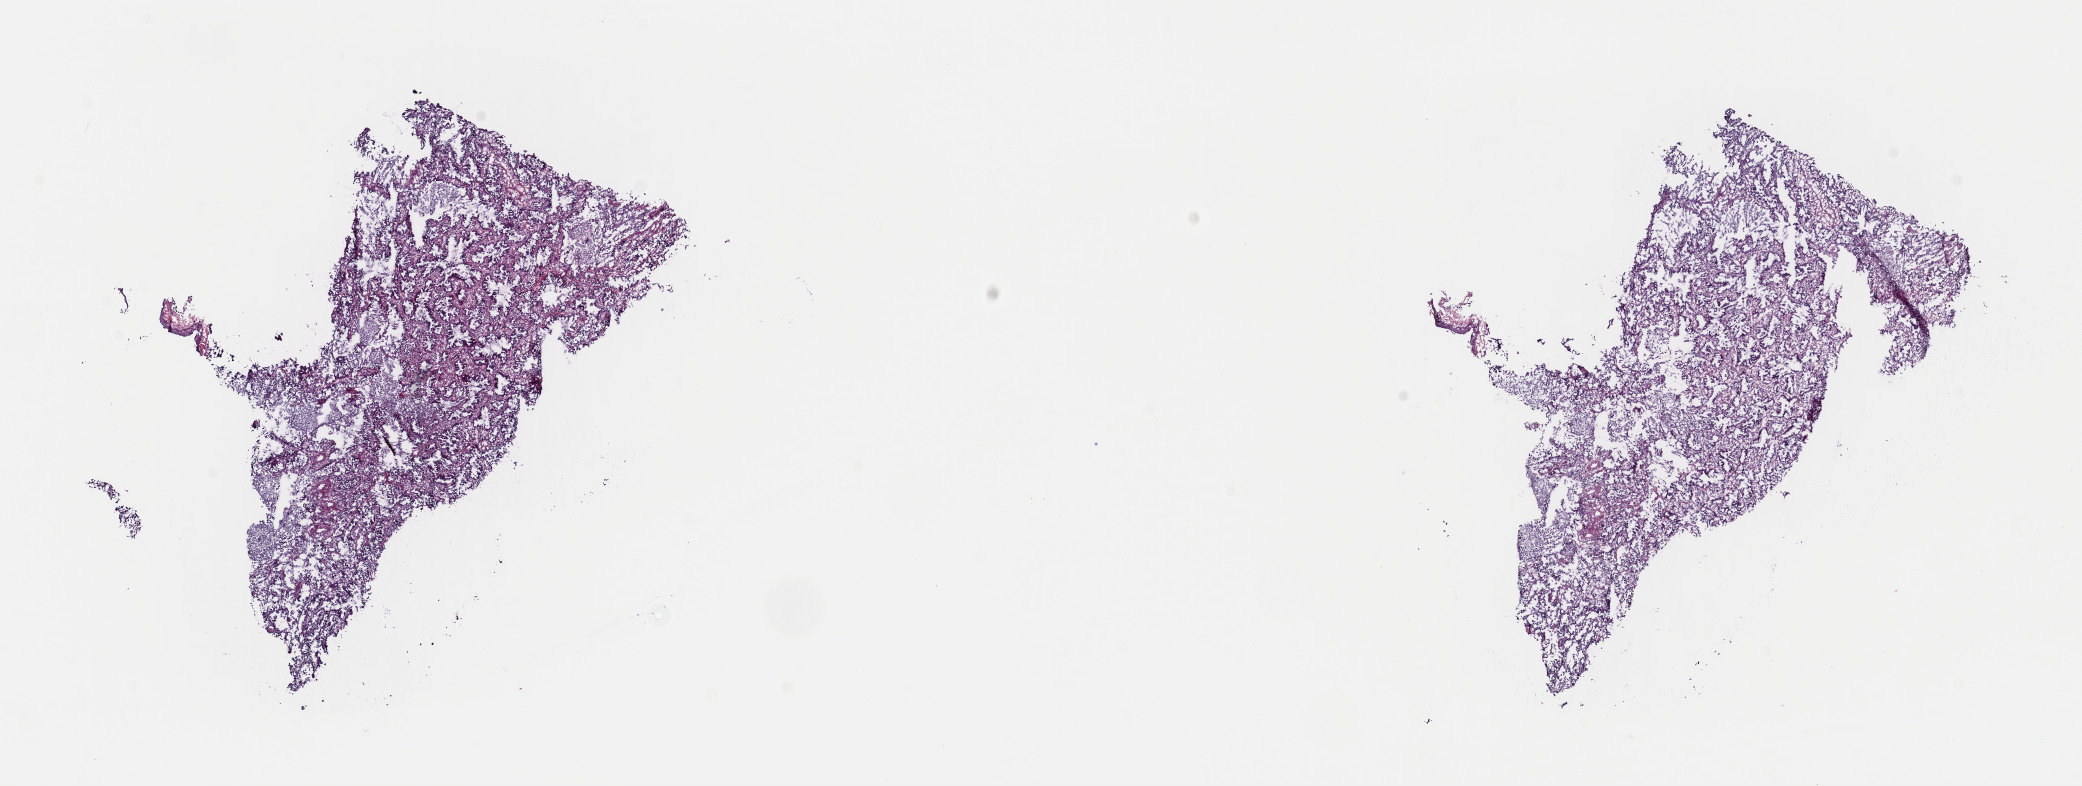
Digitized H&E-stained tissue section (whole slide) — shown as a low-resolution overview of the whole scanned area (about 16.4 x 6.2 mm). Frozen section from the top of the tissue portion. Sample: primary tumour, lung. Patient: female, age at initial diagnosis 74 years. Slide review estimates, as recorded: tumour cells 100%, tumour nuclei 75%, normal cells 0%, stromal cells 0%, necrosis 0%. Infiltration values recorded for this section: lymphocyte infiltration 2%, monocyte infiltration 5%, neutrophil infiltration 0%.
• laterality: left
• histologic diagnosis: Adenocarcinoma, NOS
• AJCC pathologic stage: IA (6th edition)
• TNM: T1 N0 MX